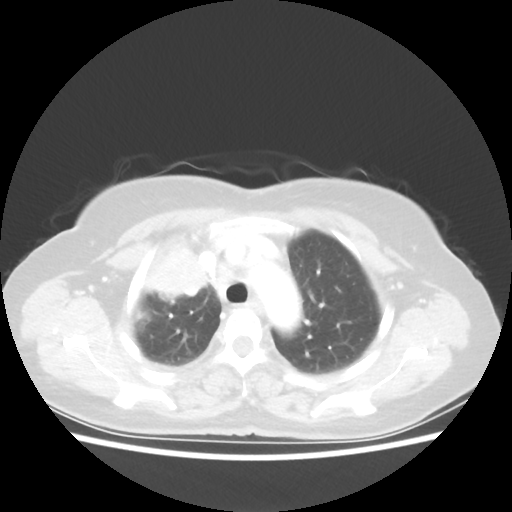
Chest CT, one axial slice; slice 42 of 55 in the series (ordered by position); reconstruction kernel STANDARD; 80 kVp; lung window (W 1500 / L -600 HU); 5 mm slice thickness; 512 × 512 image matrix. Female patient, age 62 years. From the clinical record (not read from this slice): clinical TNM (as recorded): T4 N3 M0.
Structures marked on this image (rectangle marked by the reading radiologist):
- lung tumour (recorded histology: squamous cell carcinoma): bounding box [x1, y1, x2, y2] px = [137, 241, 216, 303]